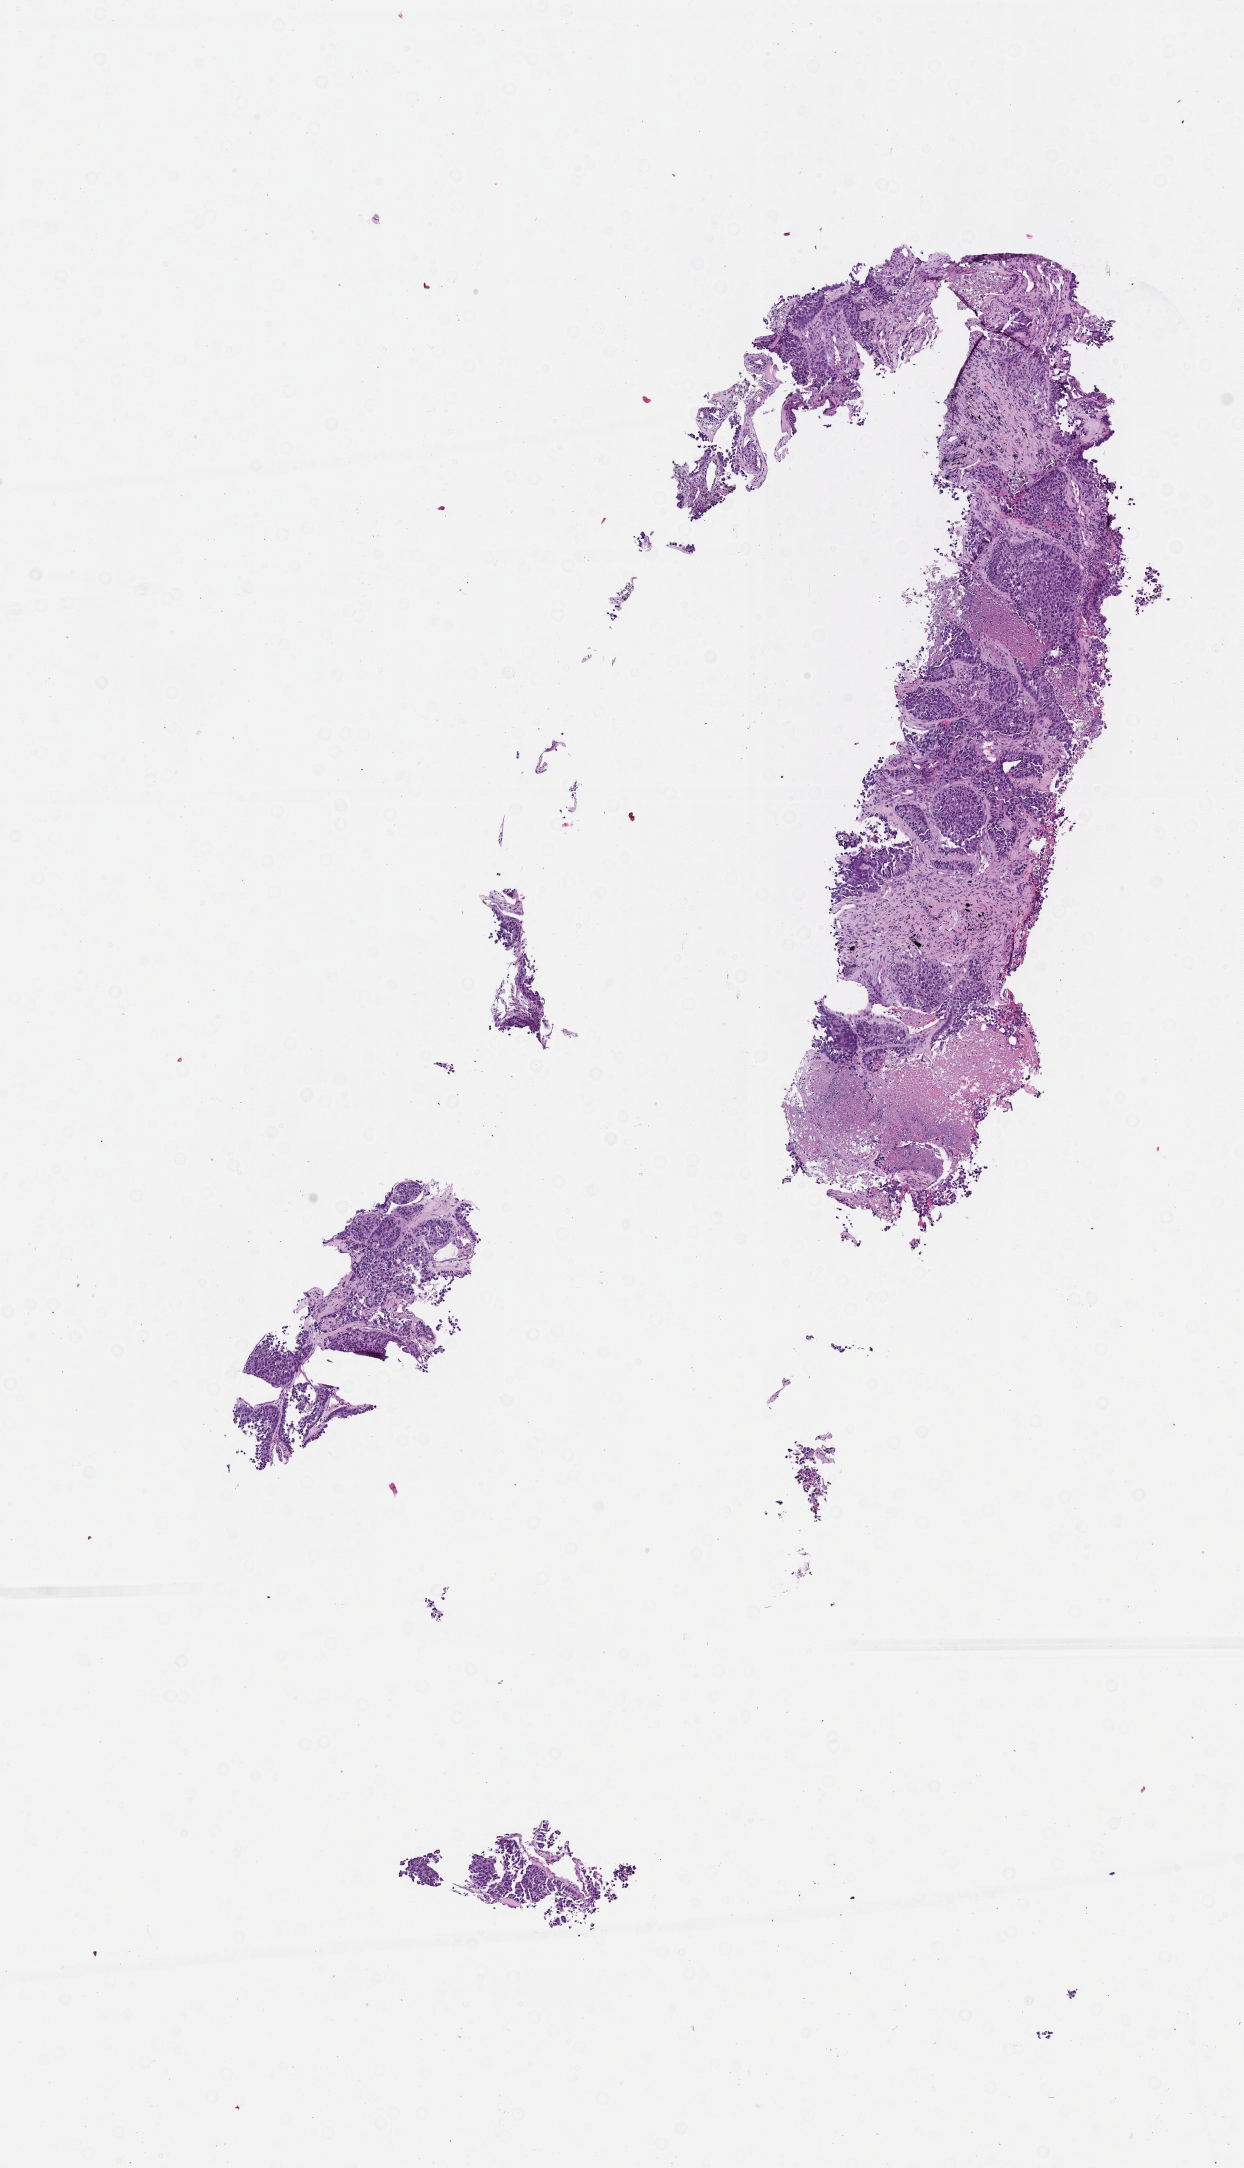
Digitized hematoxylin and eosin (H&E)-stained section, low-resolution overview of the scanned area, about 5.0 x 8.8 mm, specimen: tumor tissue, anatomic site: lung (left). Male patient, 68 years old.
Histologic diagnosis: Bronchiolo-alveolar carcinoma, non-mucinous.